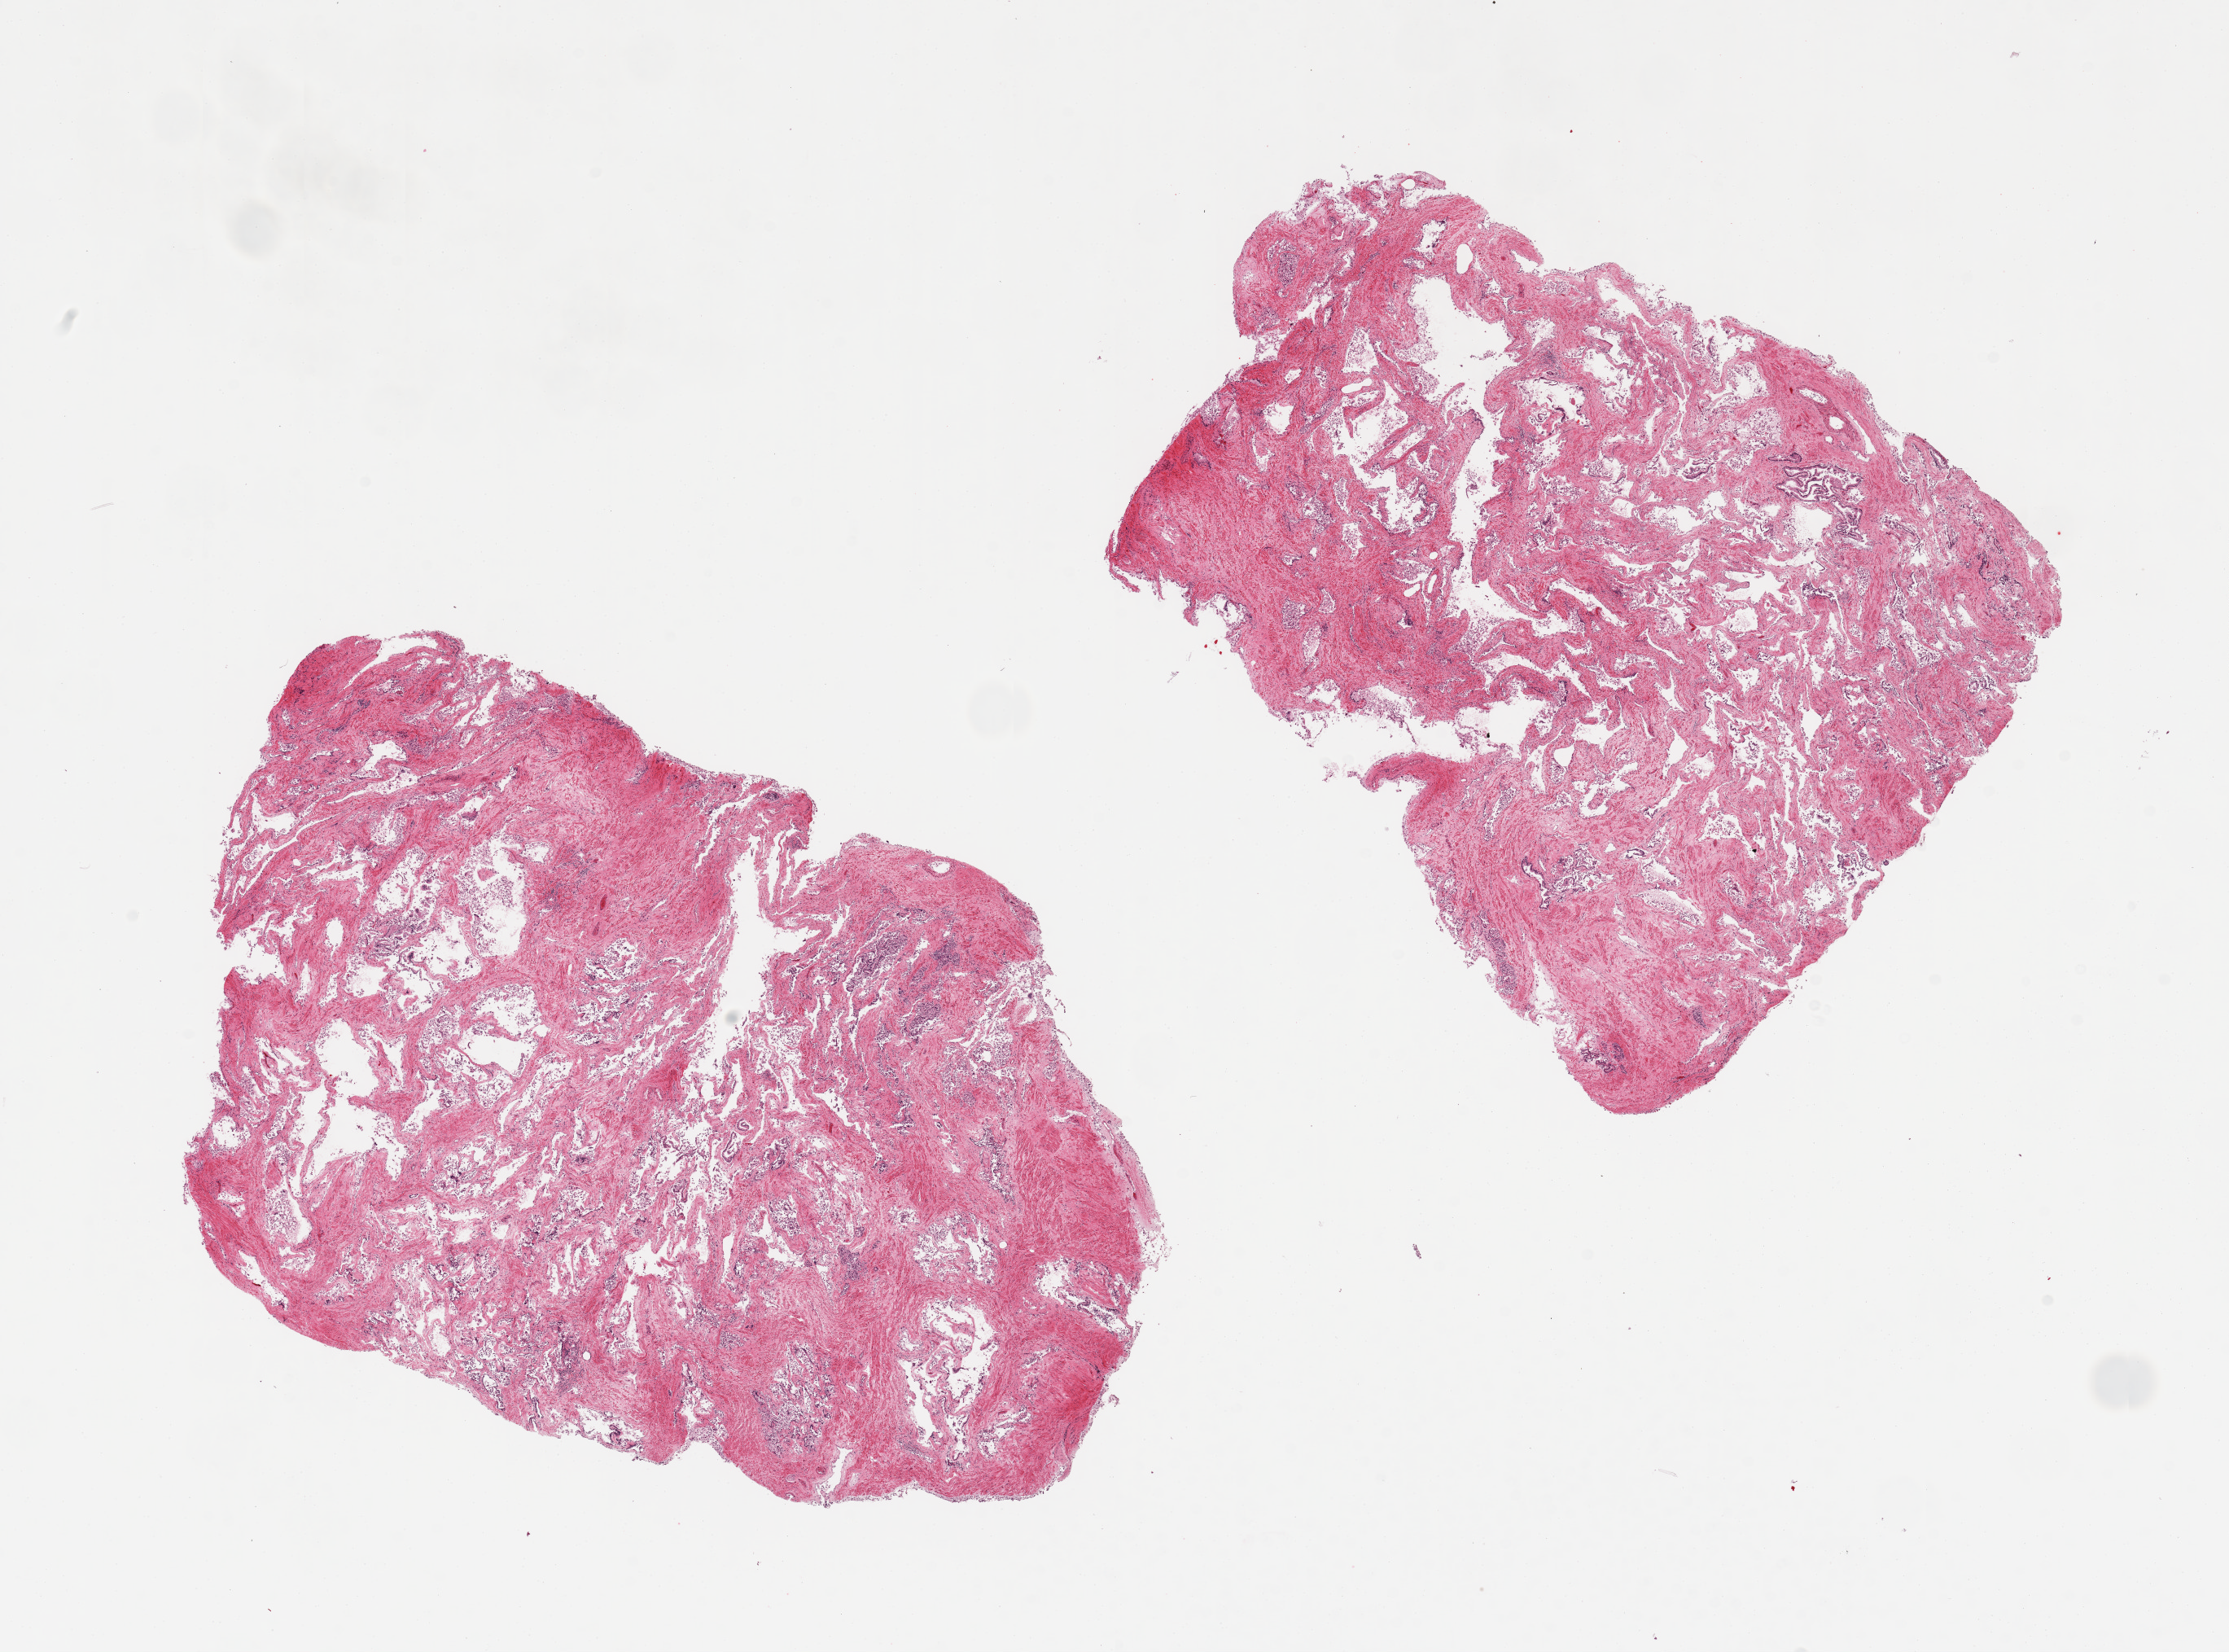
Whole-slide image, hematoxylin and eosin (H&E) stain, brightfield, whole scanned area (about 21.7 x 16.0 mm) shown as a low-resolution overview; PAXgene-fixed, paraffin-embedded tissue; sampled site (target tissue): prostate; tissue donor sample. Male donor.
Review note (as recorded): 2 pieces, glands autolyzed.